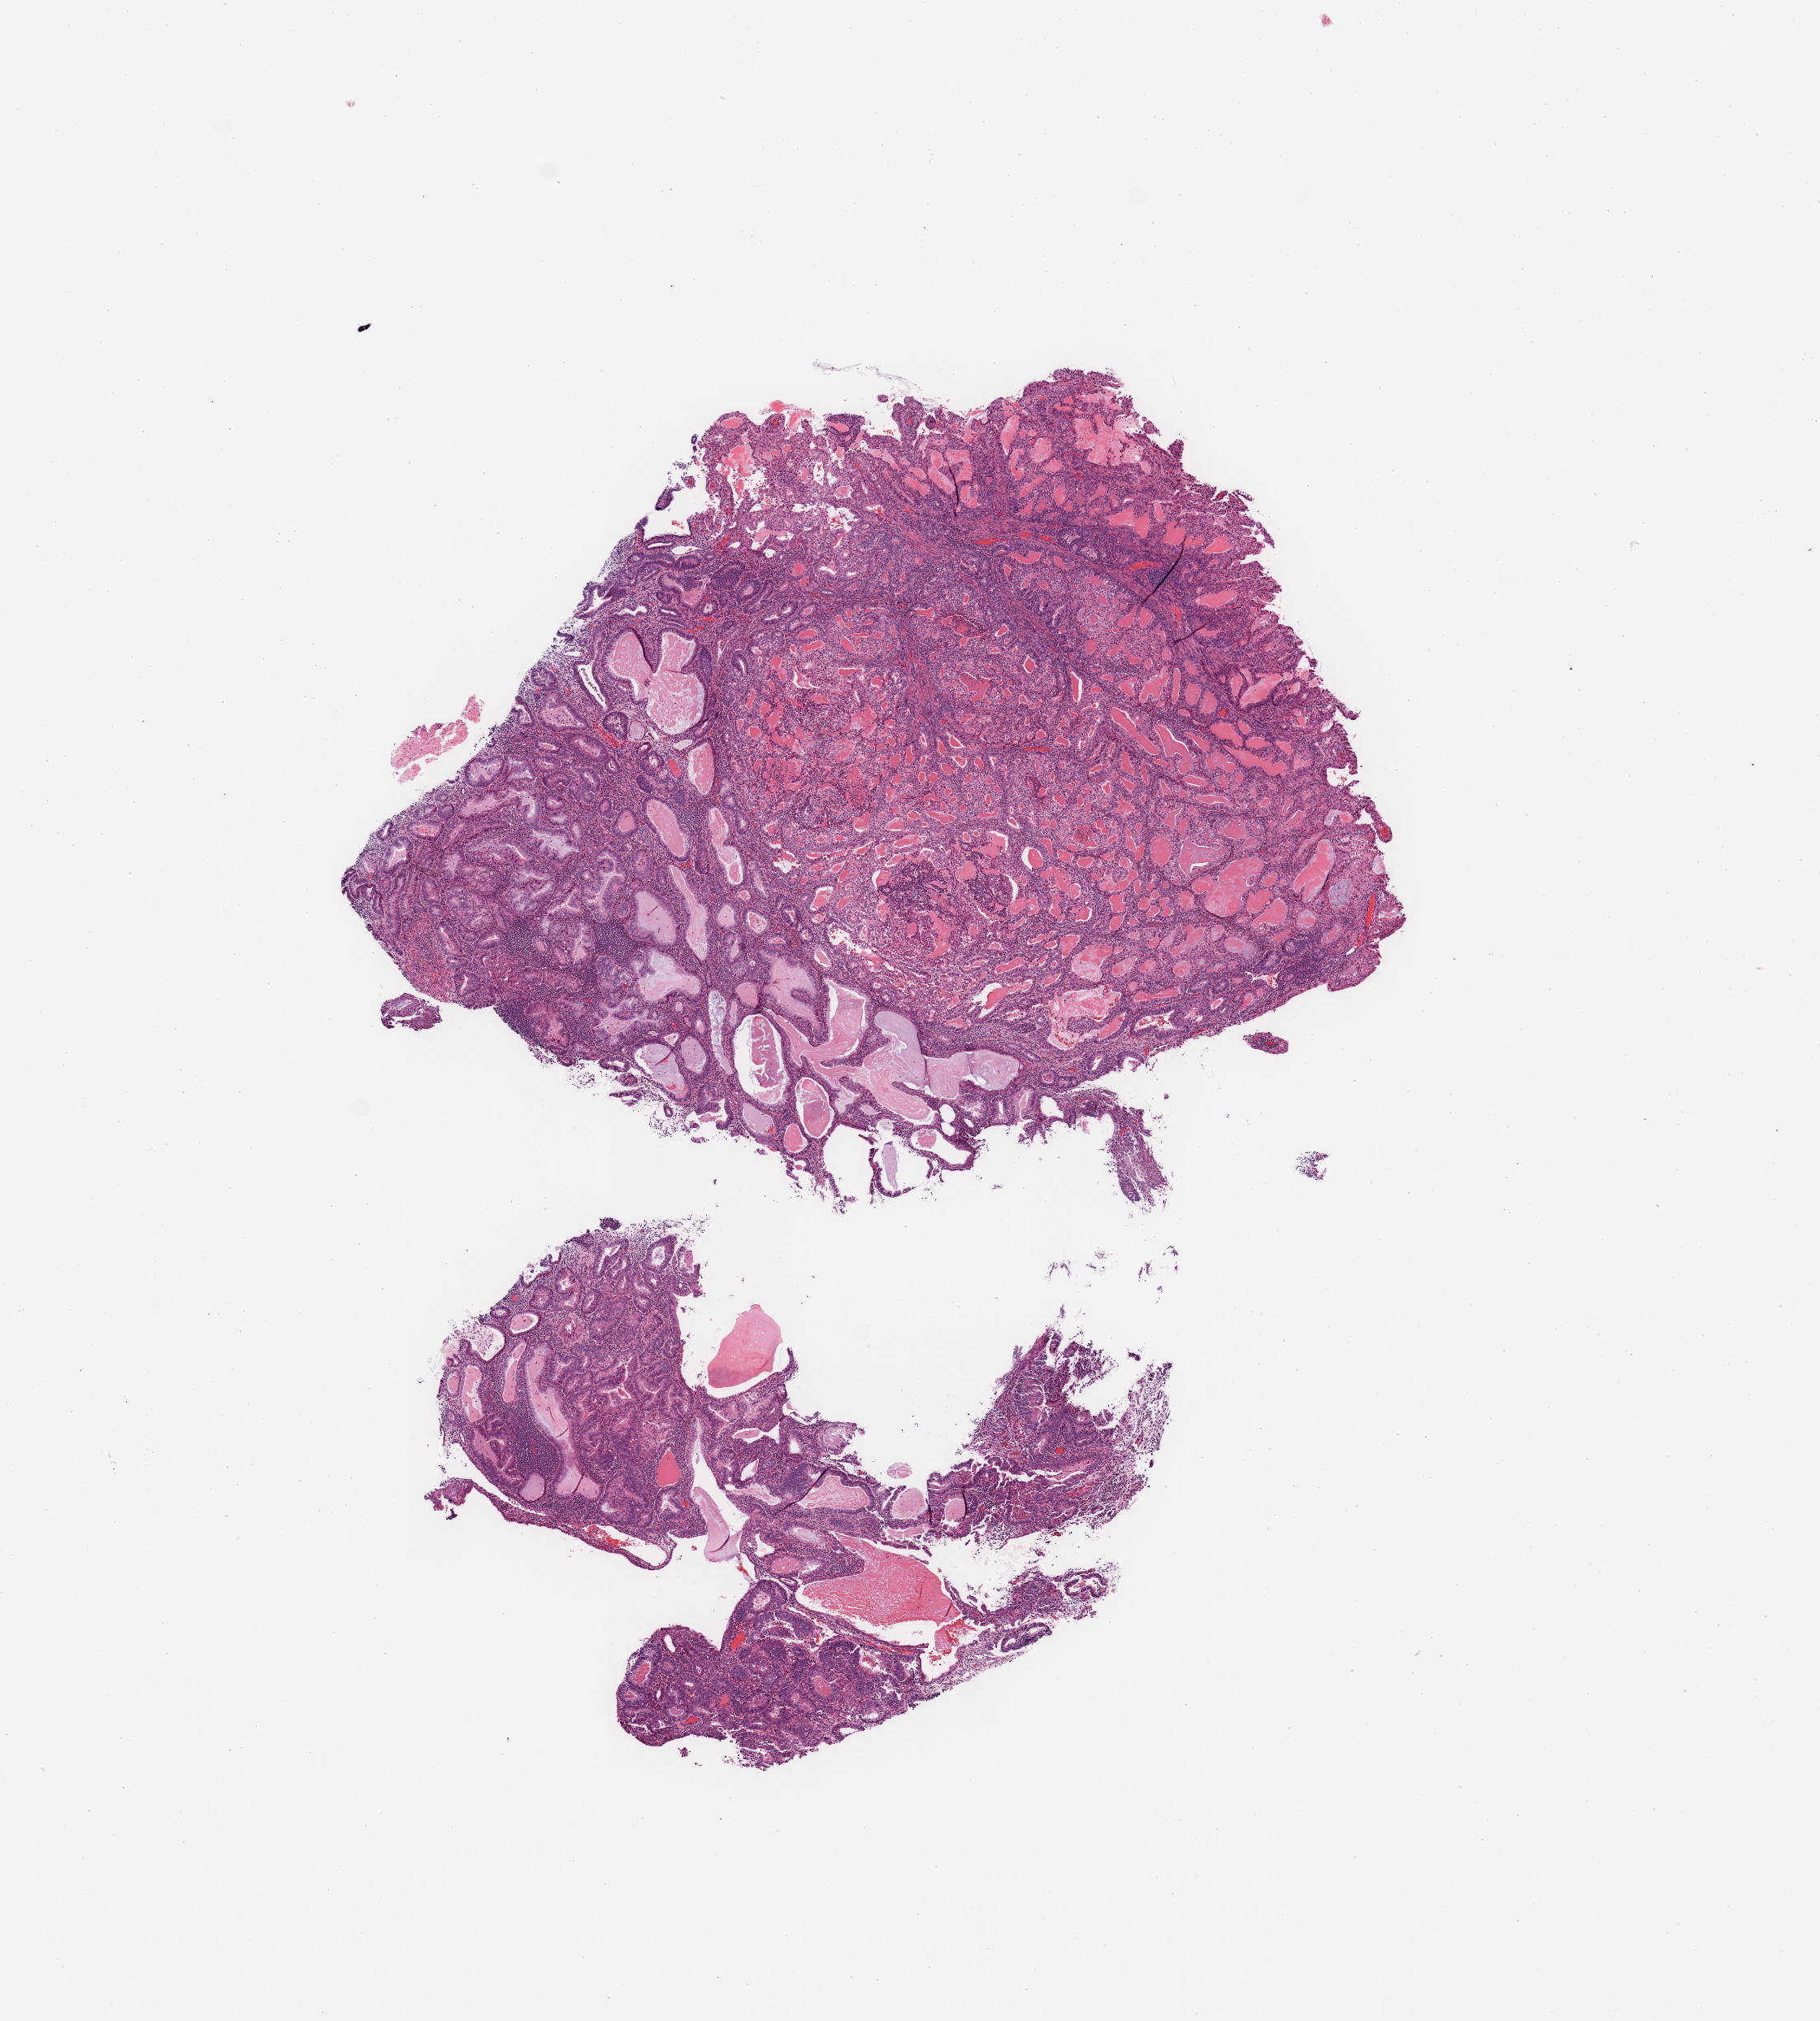
Digitized H&E-stained tissue section (whole slide) — low-resolution overview of the scanned area, about 8.9 x 9.8 mm (from a 20x scan), tumour tissue sample, sampled site: uterus. Female, 62 y/o. Histologic grade: G2 (moderately differentiated). Pathologist review of this section (percent, as recorded): tumour nuclei 90%, necrosis 0%.
• AJCC pathologic stage: I
• diagnosis: Endometrioid adenocarcinoma, NOS